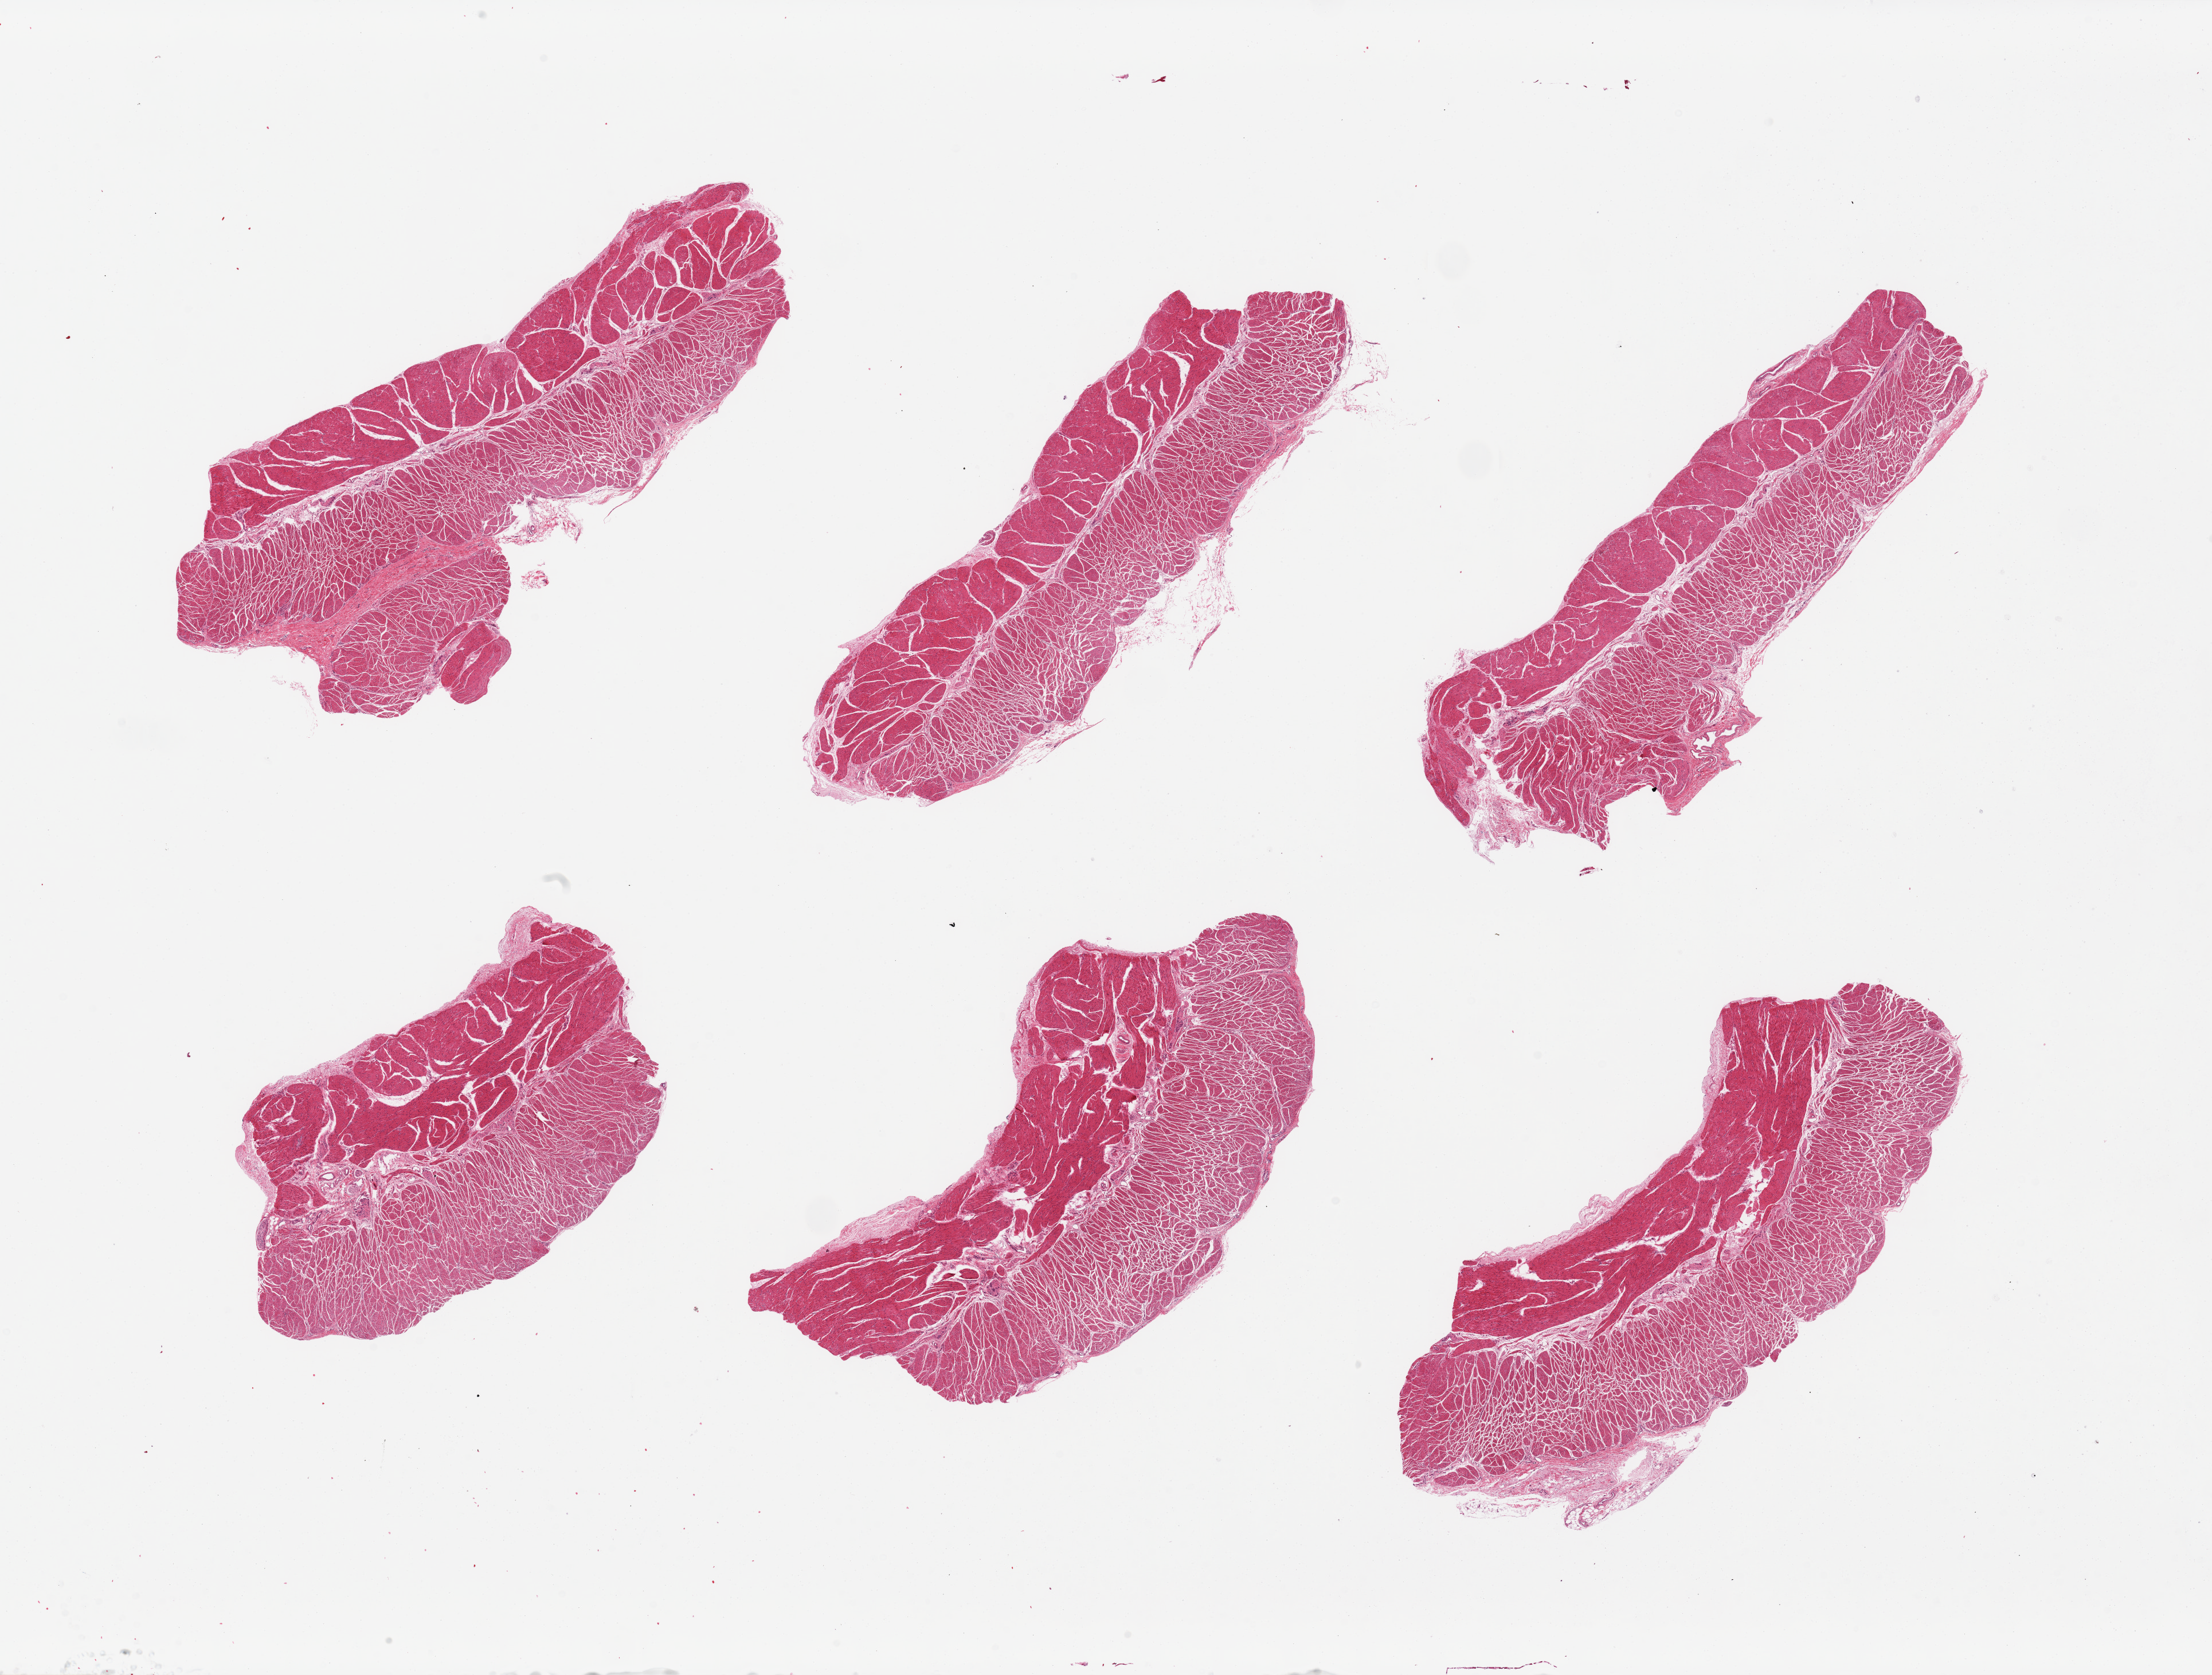
Whole-slide image, hematoxylin and eosin (H&E) stain, whole scanned area (about 30.5 x 23.1 mm) shown as a low-resolution overview, PAXgene-fixed, paraffin-embedded tissue, section of esophageal muscle (target tissue), donor tissue sample.
* pathologist's review note for this sample: 6 pieces well dissected